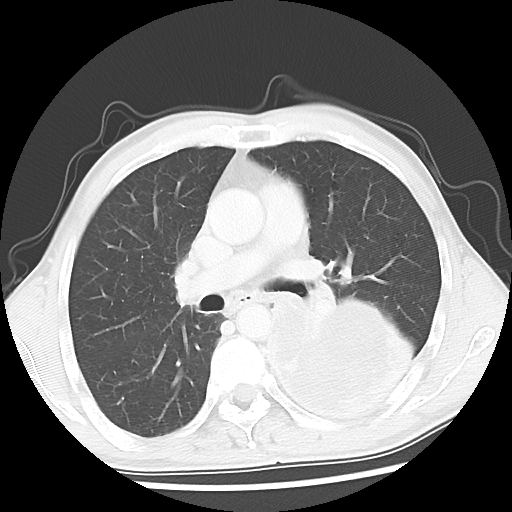
Chest CT, one axial slice; slice 29 of 52 in the series (ordered by position); reconstruction kernel LUNG; 120 kVp; lung window (W 1500 / L -600 HU); 512 × 512 image matrix, field of view 318 × 318 mm. Male patient, age 60 years. Case-level facts recorded for this patient, not image findings: clinical TNM (as recorded): T4 N0 M0.
Annotated regions visible in this slice (rectangle marked by the reading radiologist):
- lung tumour (recorded histology: squamous cell carcinoma): bounding box (x1, y1, x2, y2) in pixels: (263, 295, 409, 421)